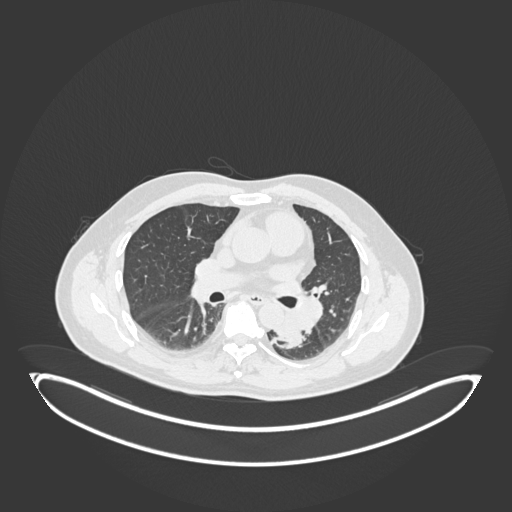
Chest CT, one axial slice; position 110 of 258 along the scan axis; reconstruction kernel B30f; 120 kVp; lung window (W 1500 / L -600 HU); 1 mm slice thickness; 512 × 512 image matrix. Patient: male, 54 years. Case-level facts recorded for this patient, not image findings: clinical TNM (as recorded): T3 N0 M0.
Outlined on this slice (rectangle marked by the reading radiologist):
- lung tumour (recorded histology: squamous cell carcinoma): bounding box [x1, y1, x2, y2] px = [275, 309, 308, 352]